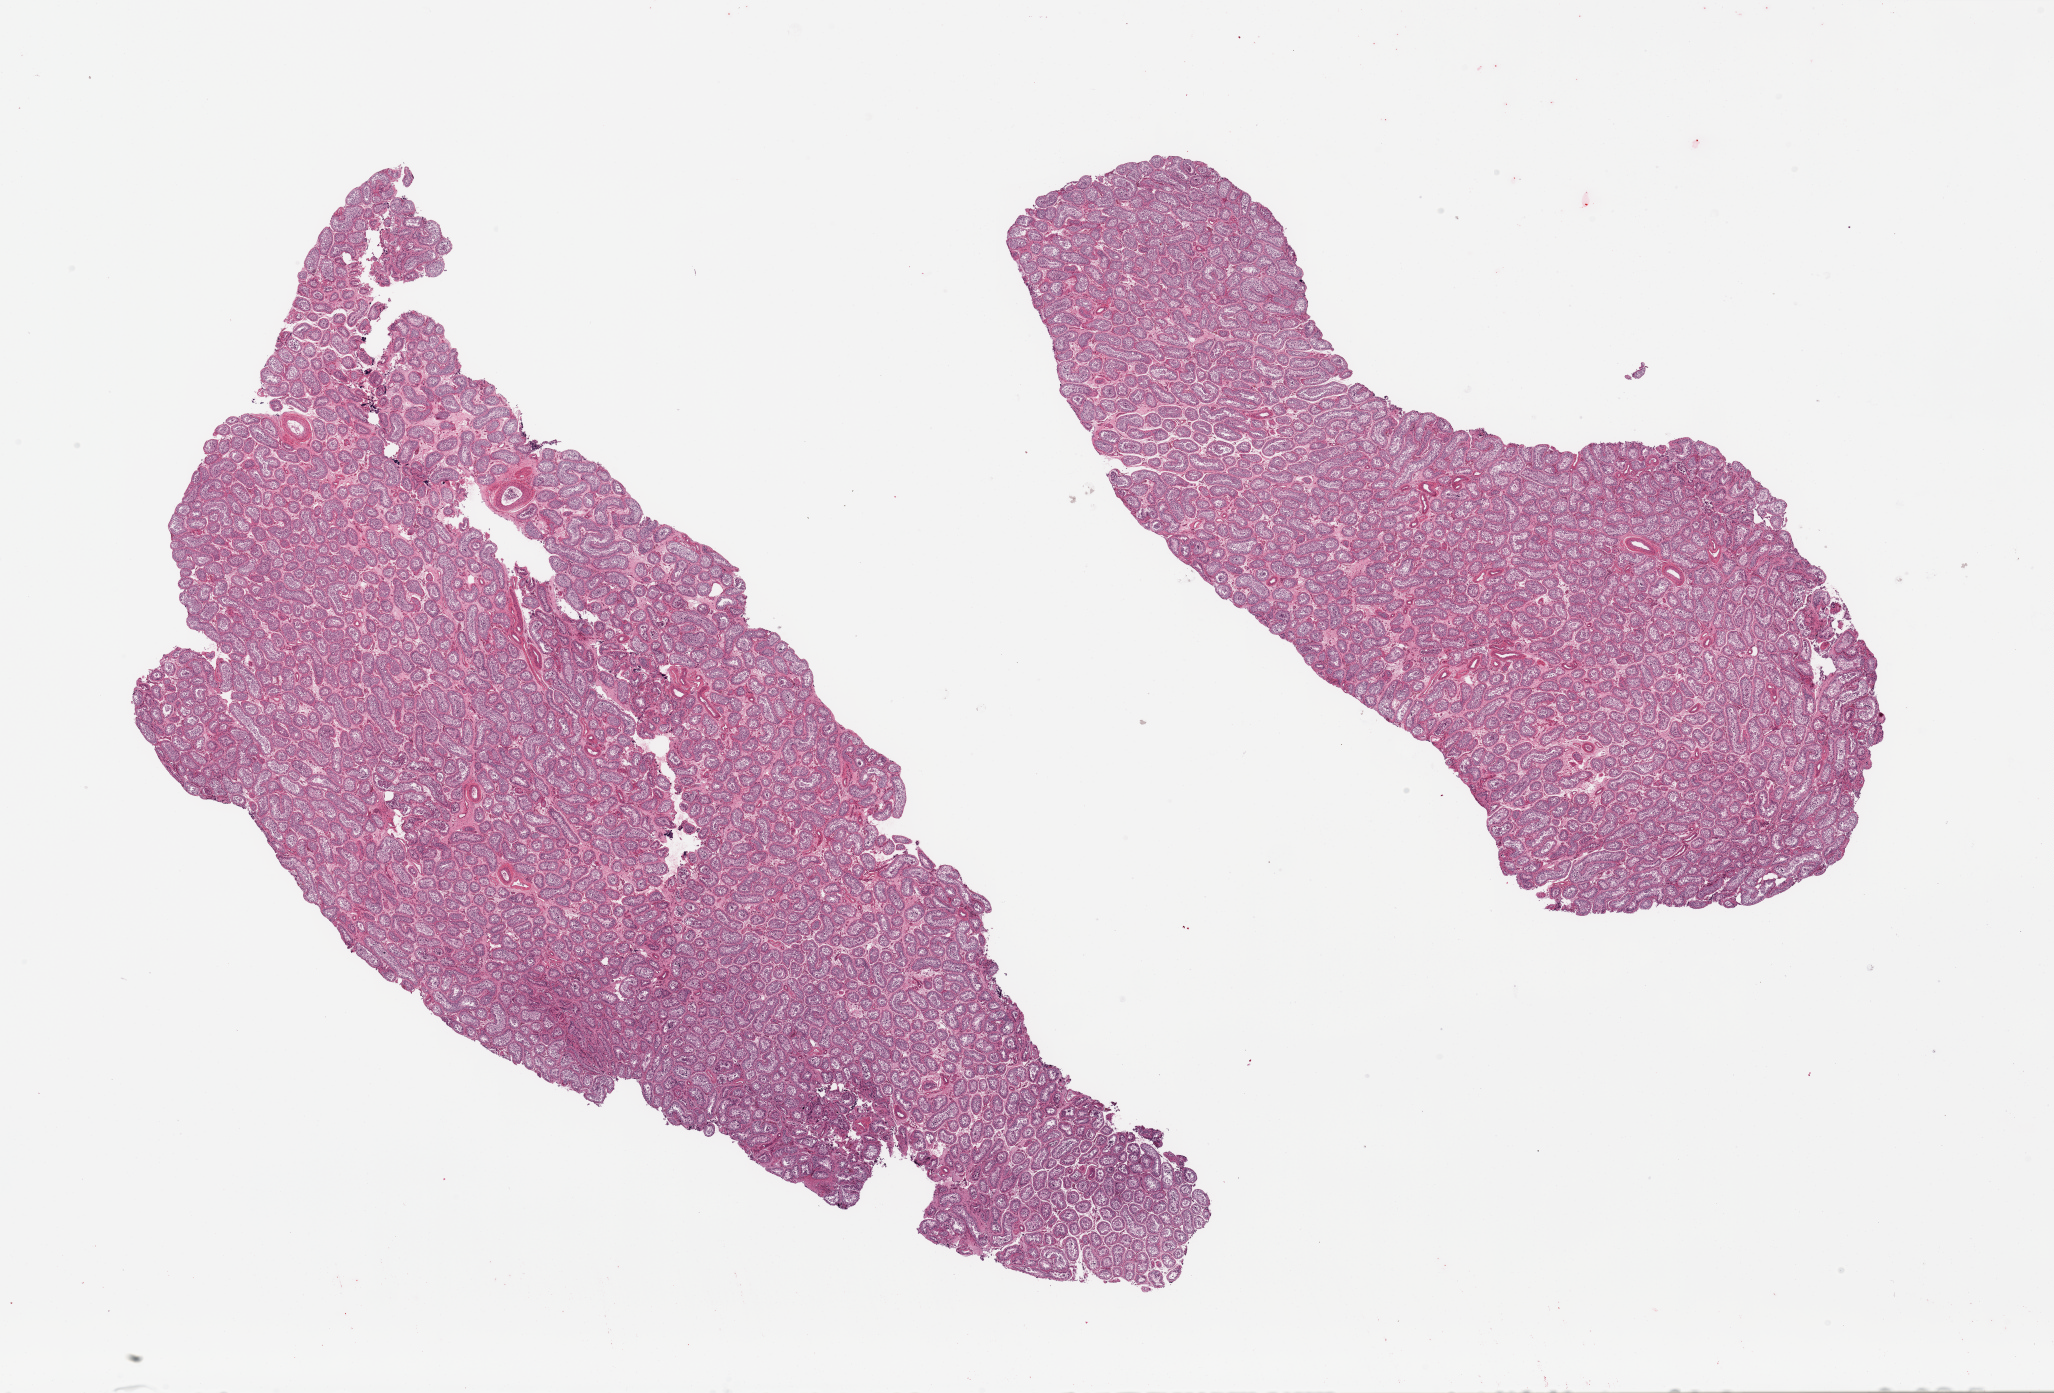
Digitized H&E-stained section — a low-resolution overview of the entire scanned area, about 32.5 x 22.0 mm; PAXgene-fixed, paraffin-embedded tissue; section of testis (target tissue); tissue donor sample.
Pathologist's review note for this sample: 2 pieces, spermatogenesis is present.